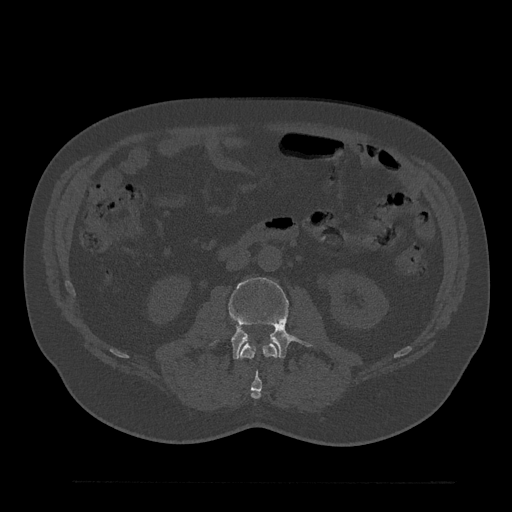
CT including the spine, one axial slice; slice 59 of 797 in the series (ordered by position); reconstruction kernel Br40s/3; 120 kVp; bone window (W 1800 / L 400 HU); 0.5 mm slice thickness; 512 × 512 image matrix, field of view 430 × 430 mm. Patient: male, 61 years. Case-level facts recorded for this patient, not image findings: primary cancer: prostate.
Structures marked on this image (semi-automatically segmented with operator editing):
- L2 vertebra: box from (x=239, y=342) to (x=278, y=399) px
- L3 vertebra: (x=228, y=277)–(x=310, y=359)